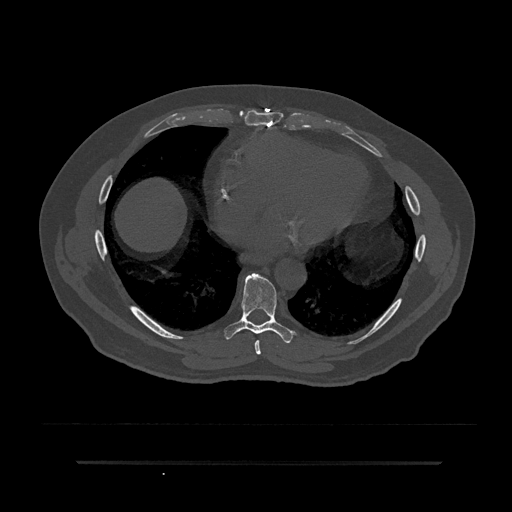
CT including the spine, one axial slice. Position 433 of 797 along the scan axis. 120 kVp. Bone window (W 1800 / L 400 HU). 0.5 mm slice thickness. 512 × 512 image matrix, field of view 464 × 464 mm. Patient: male, 59 years. Case-level facts recorded for this patient, not image findings: primary cancer: bile ducts.
Outlined on this slice (semi-automatically segmented with operator editing):
- T7 vertebra: bounding box <255,340,261,355> (left, top, right, bottom; pixels)
- T8 vertebra: <224,273,295,343>